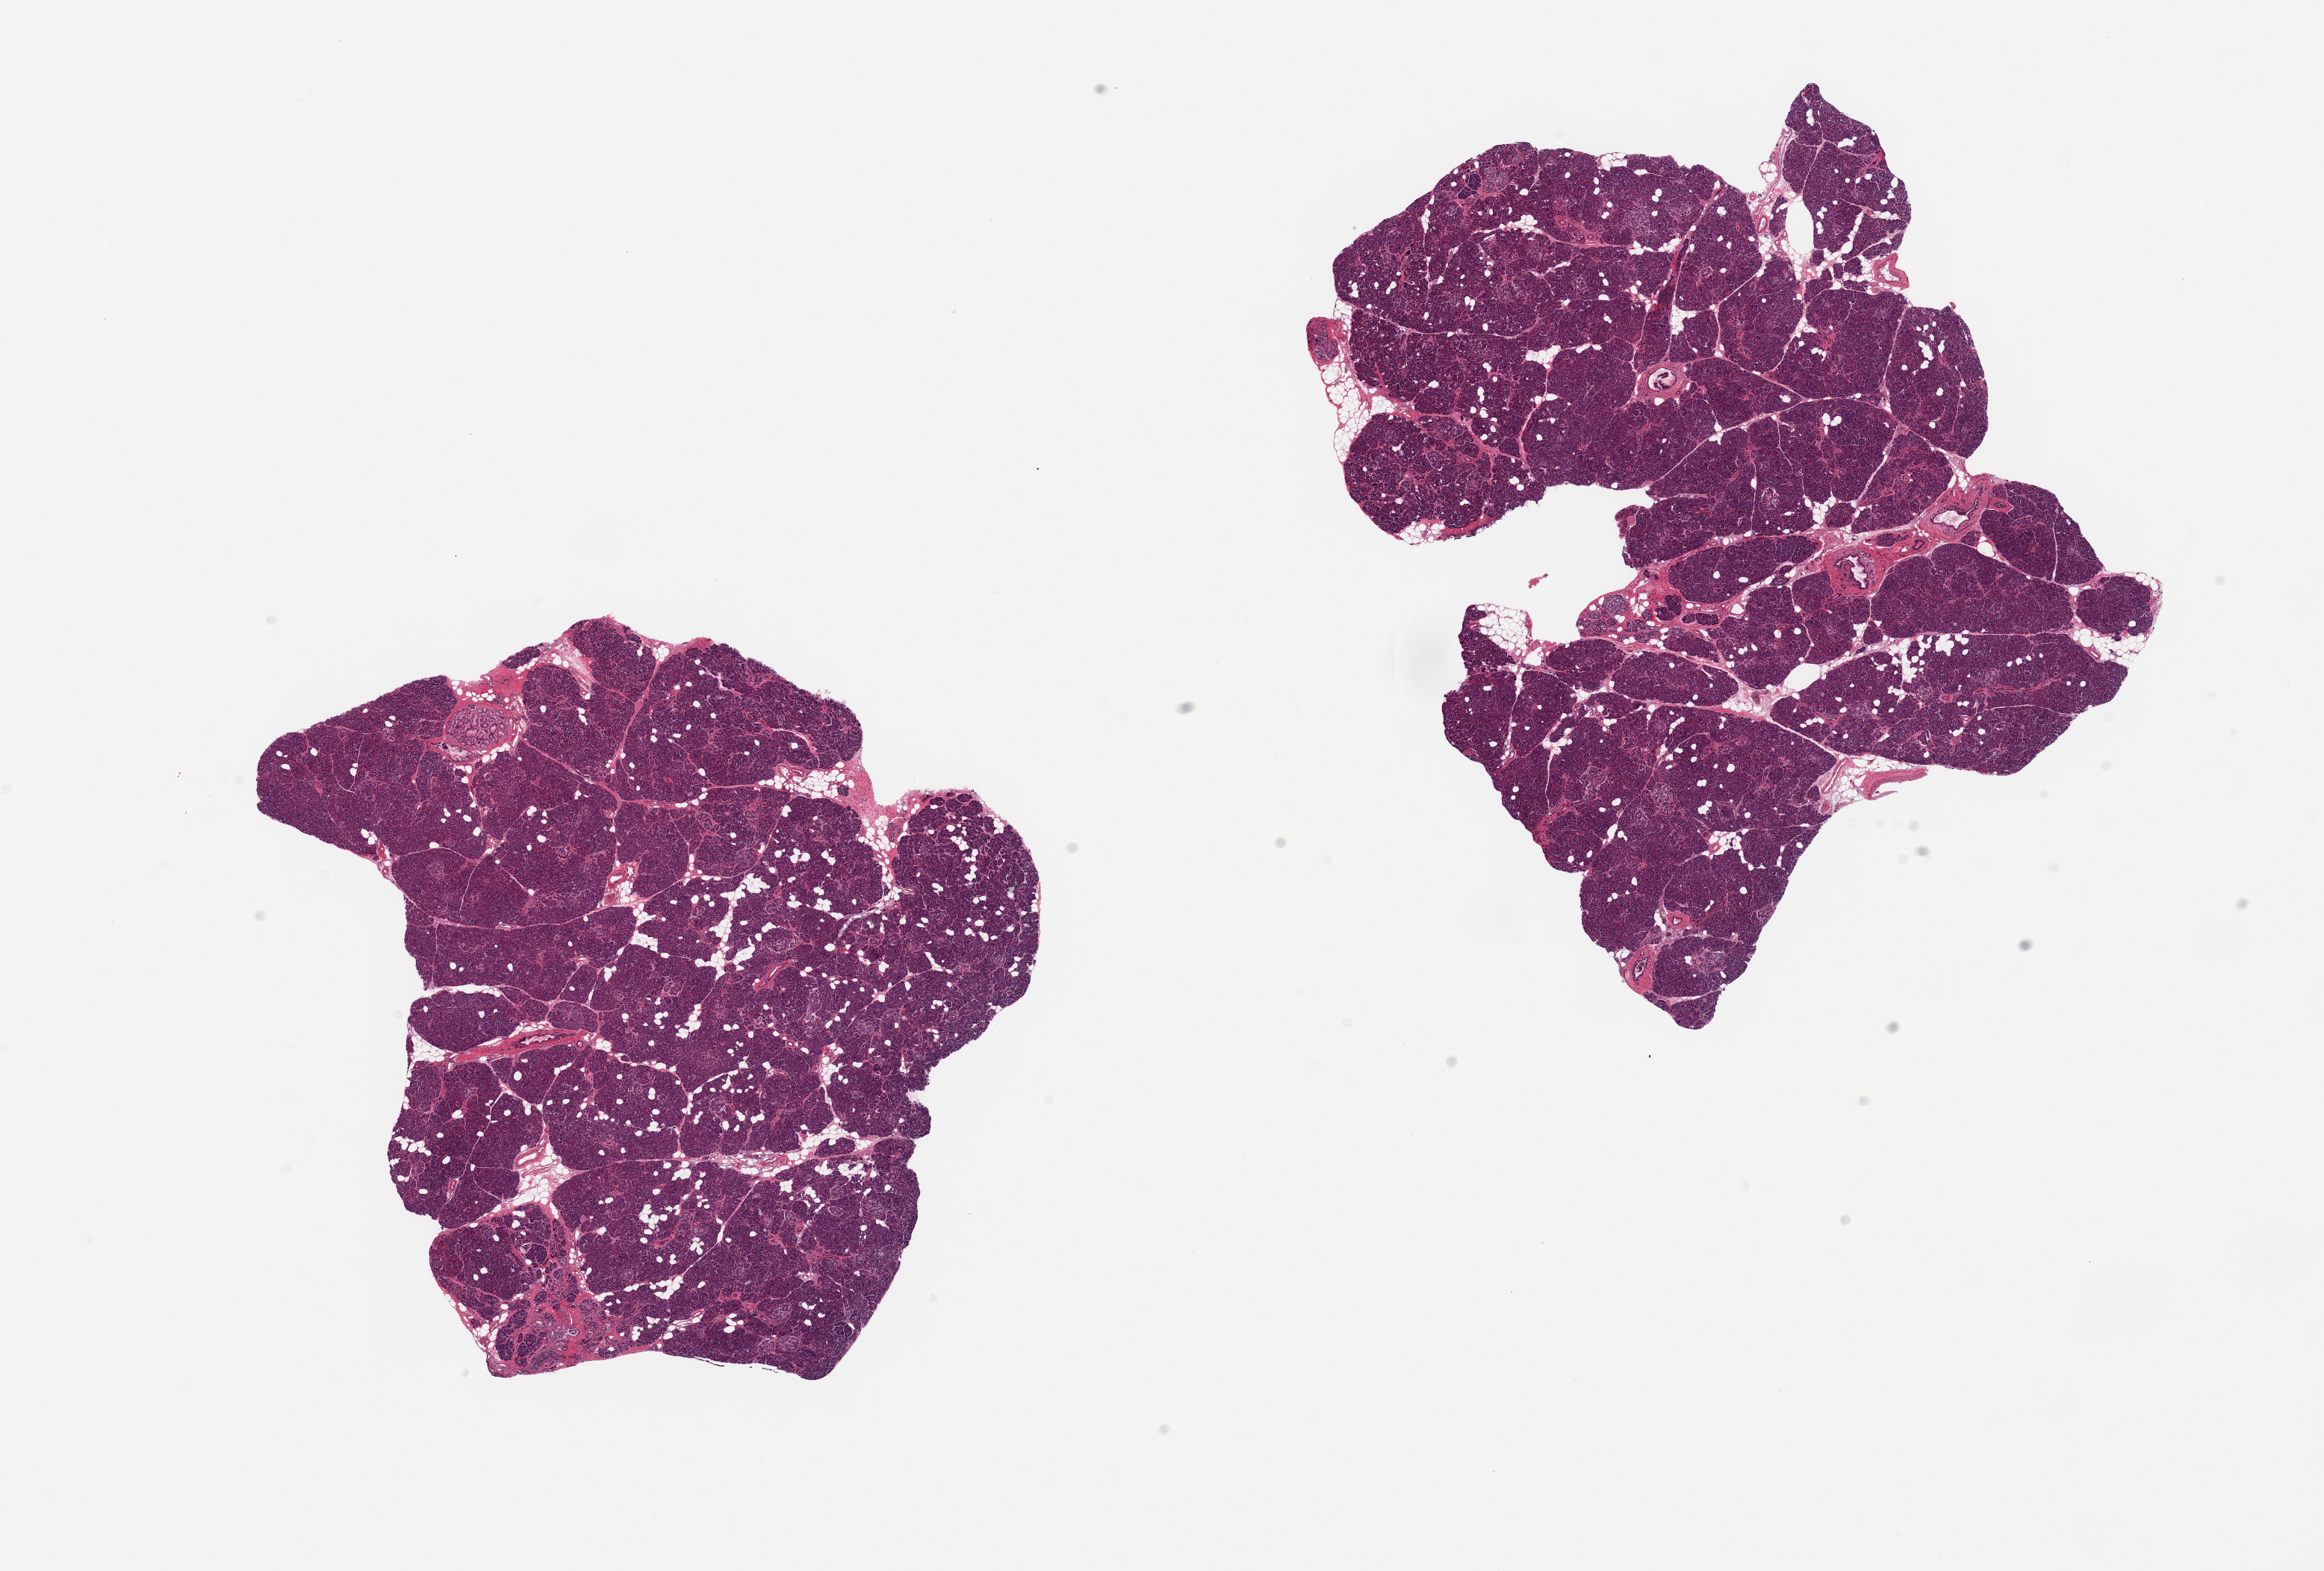
Hematoxylin and eosin (H&E) whole-slide image, a low-resolution overview of the entire scanned area, about 24.6 x 16.6 mm (acquisition: 20x scan), PAXgene-fixed, paraffin-embedded tissue, section of pancreas (target tissue), donor tissue sample. Donor: female.
Reviewer comment on this tissue sample: 2 pieces; 10% internal fat; 2 foci (0.75 & 0.3 mm) PanIN 1.